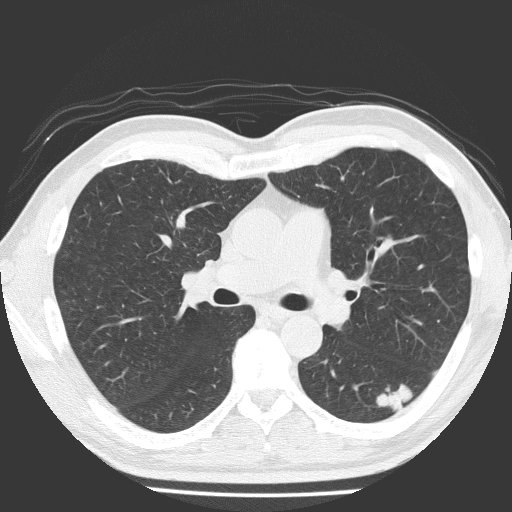
Low-dose screening chest CT, one axial slice. Slice 109 of 184 in the series (ordered by position). 120 kVp. Lung window (W 1500 / L -600 HU). 2 mm slice thickness. 512 × 512 image matrix, field of view 348 × 348 mm.
Outlined on this slice (expert manual segmentation):
- lesion 1 (tumor, lower lobe of left lung): bounding box (x1, y1, x2, y2) in pixels: (376, 384, 413, 413)